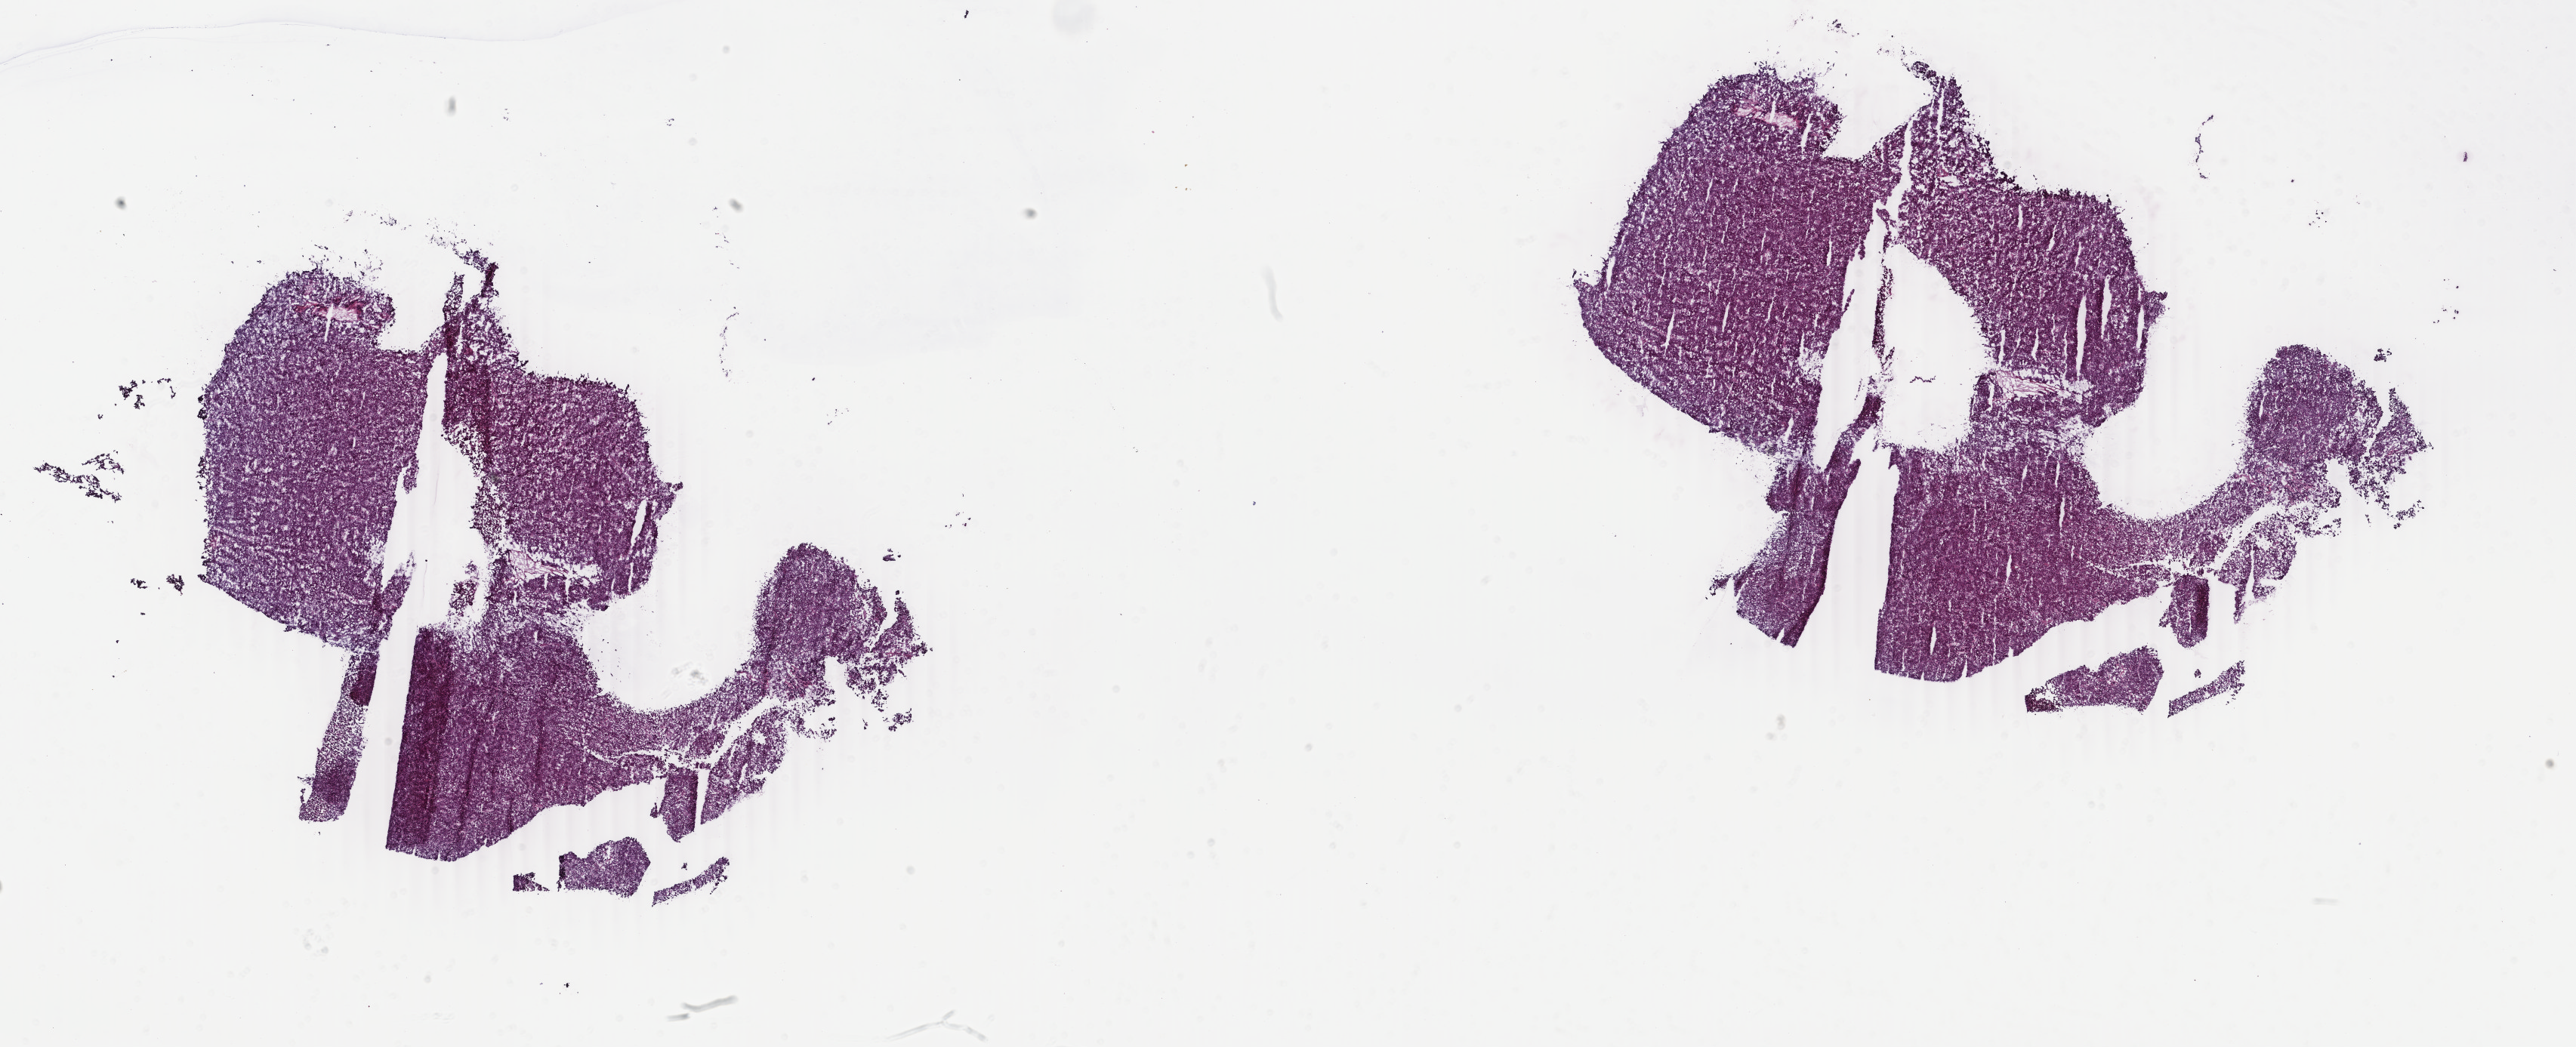
Whole-slide histology image, Hematoxylin and eosin (H&E) stained — a low-resolution overview of the entire scanned area, about 27.1 x 11.0 mm (from a 40x scan); frozen section from the bottom of the tissue portion; liver, primary tumour sample. Patient: female, age at initial diagnosis 62 years.
Diagnosis: Hepatocellular carcinoma, NOS.